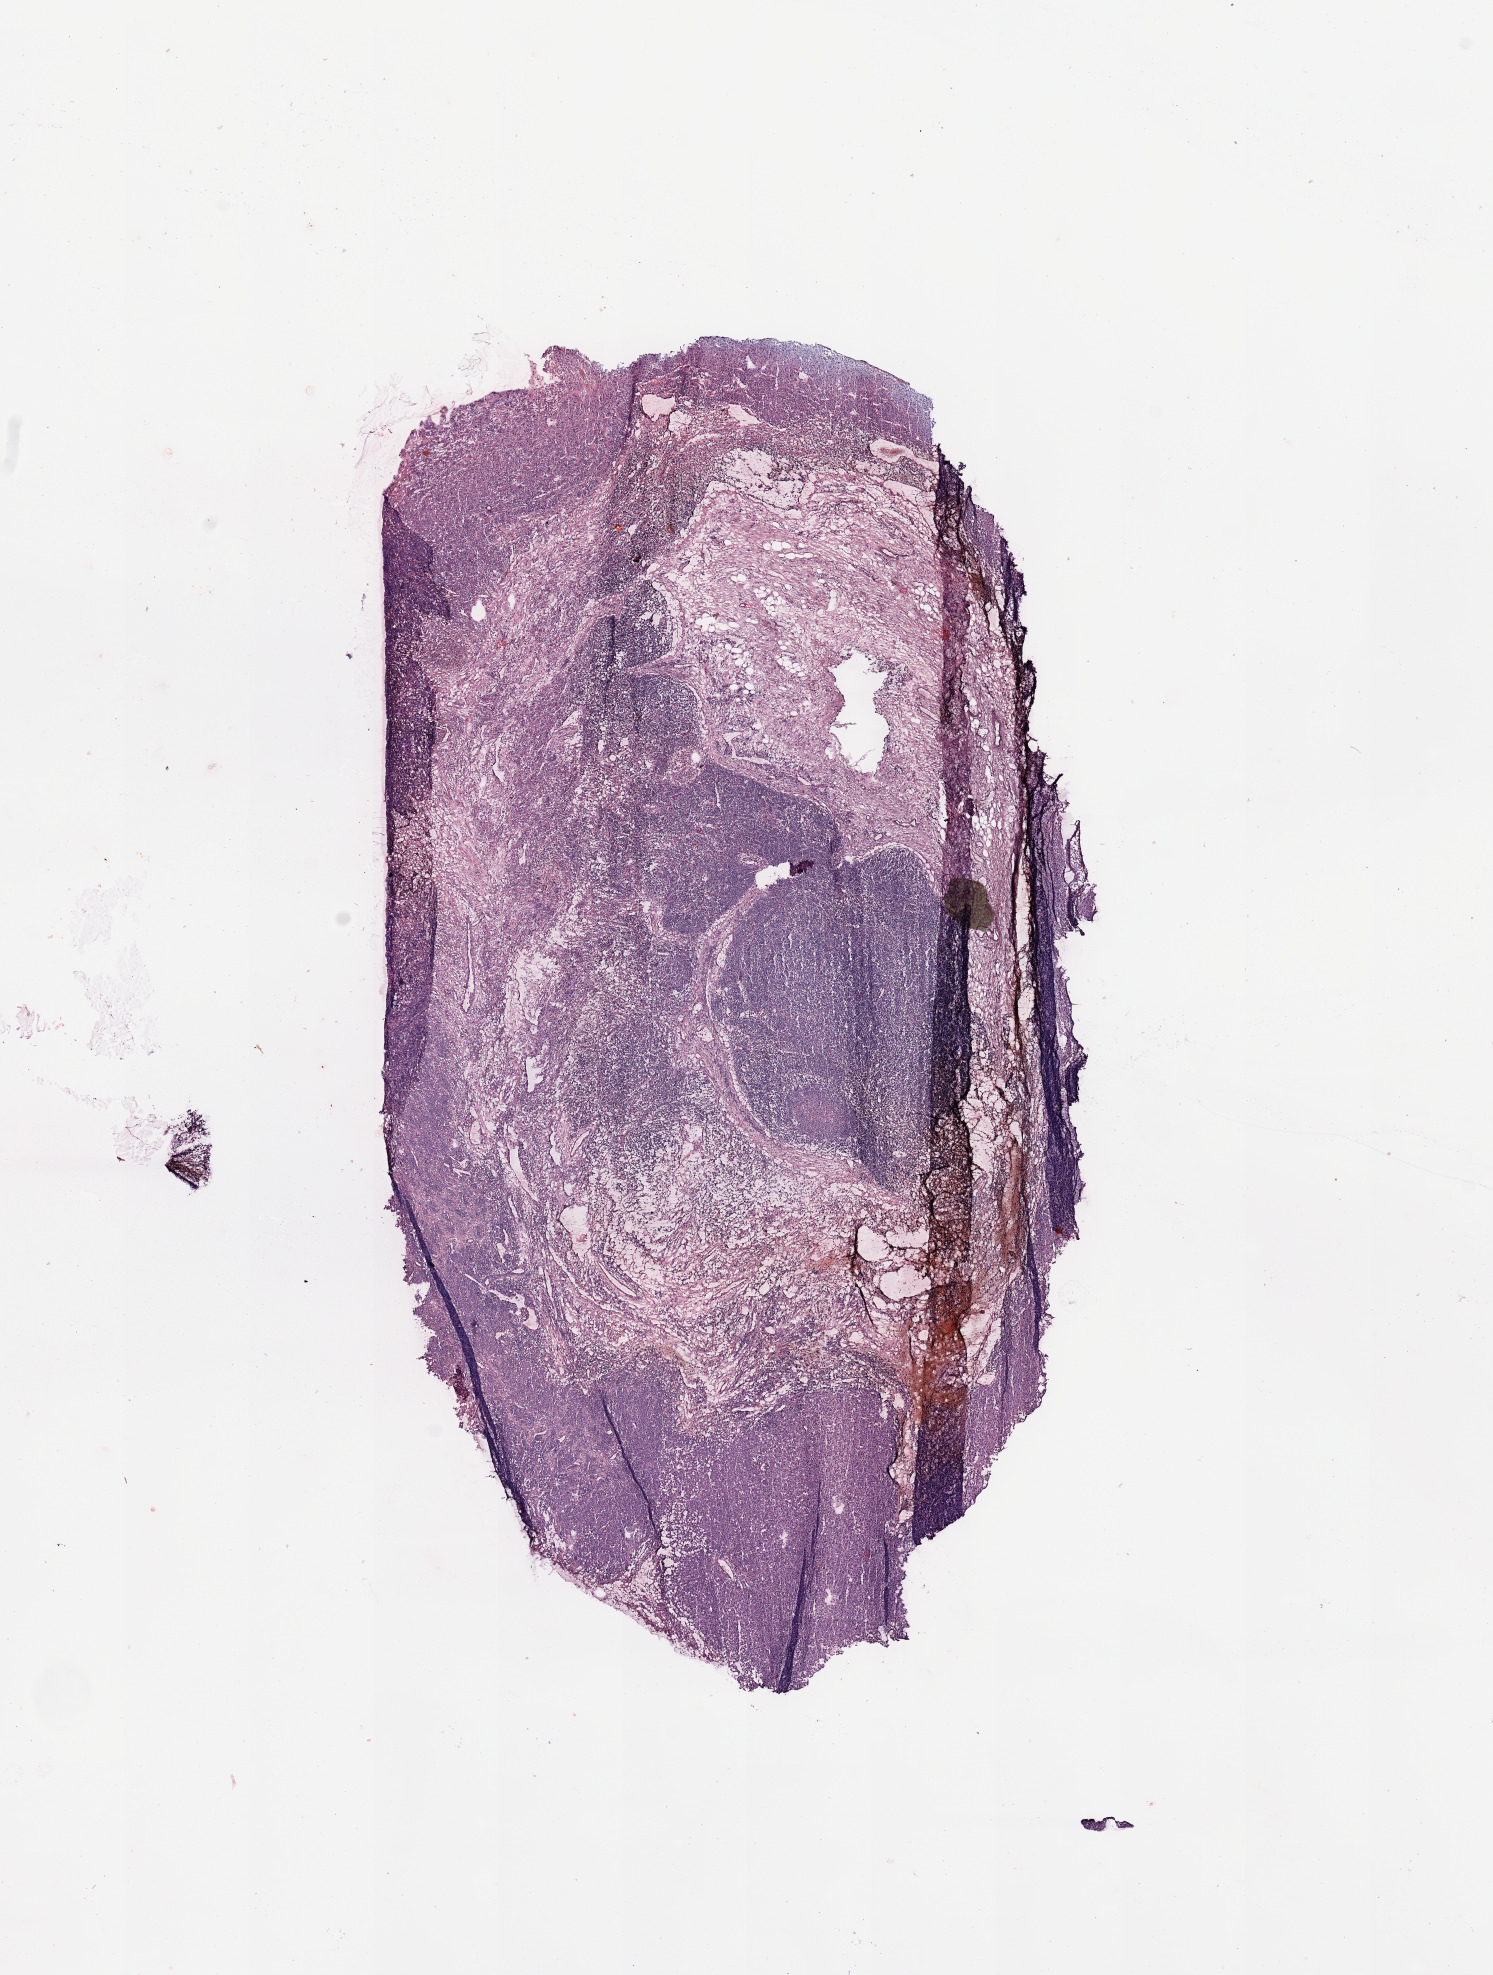
Digitized H&E-stained tissue section (whole slide) — low-resolution overview of the scanned area, about 11.8 x 15.6 mm (from a 20x scan); melanoma tumour tissue; sampled site not recorded. 66-year-old male patient.
Patient diagnosis (cohort enrolment): cutaneous melanoma (skin).